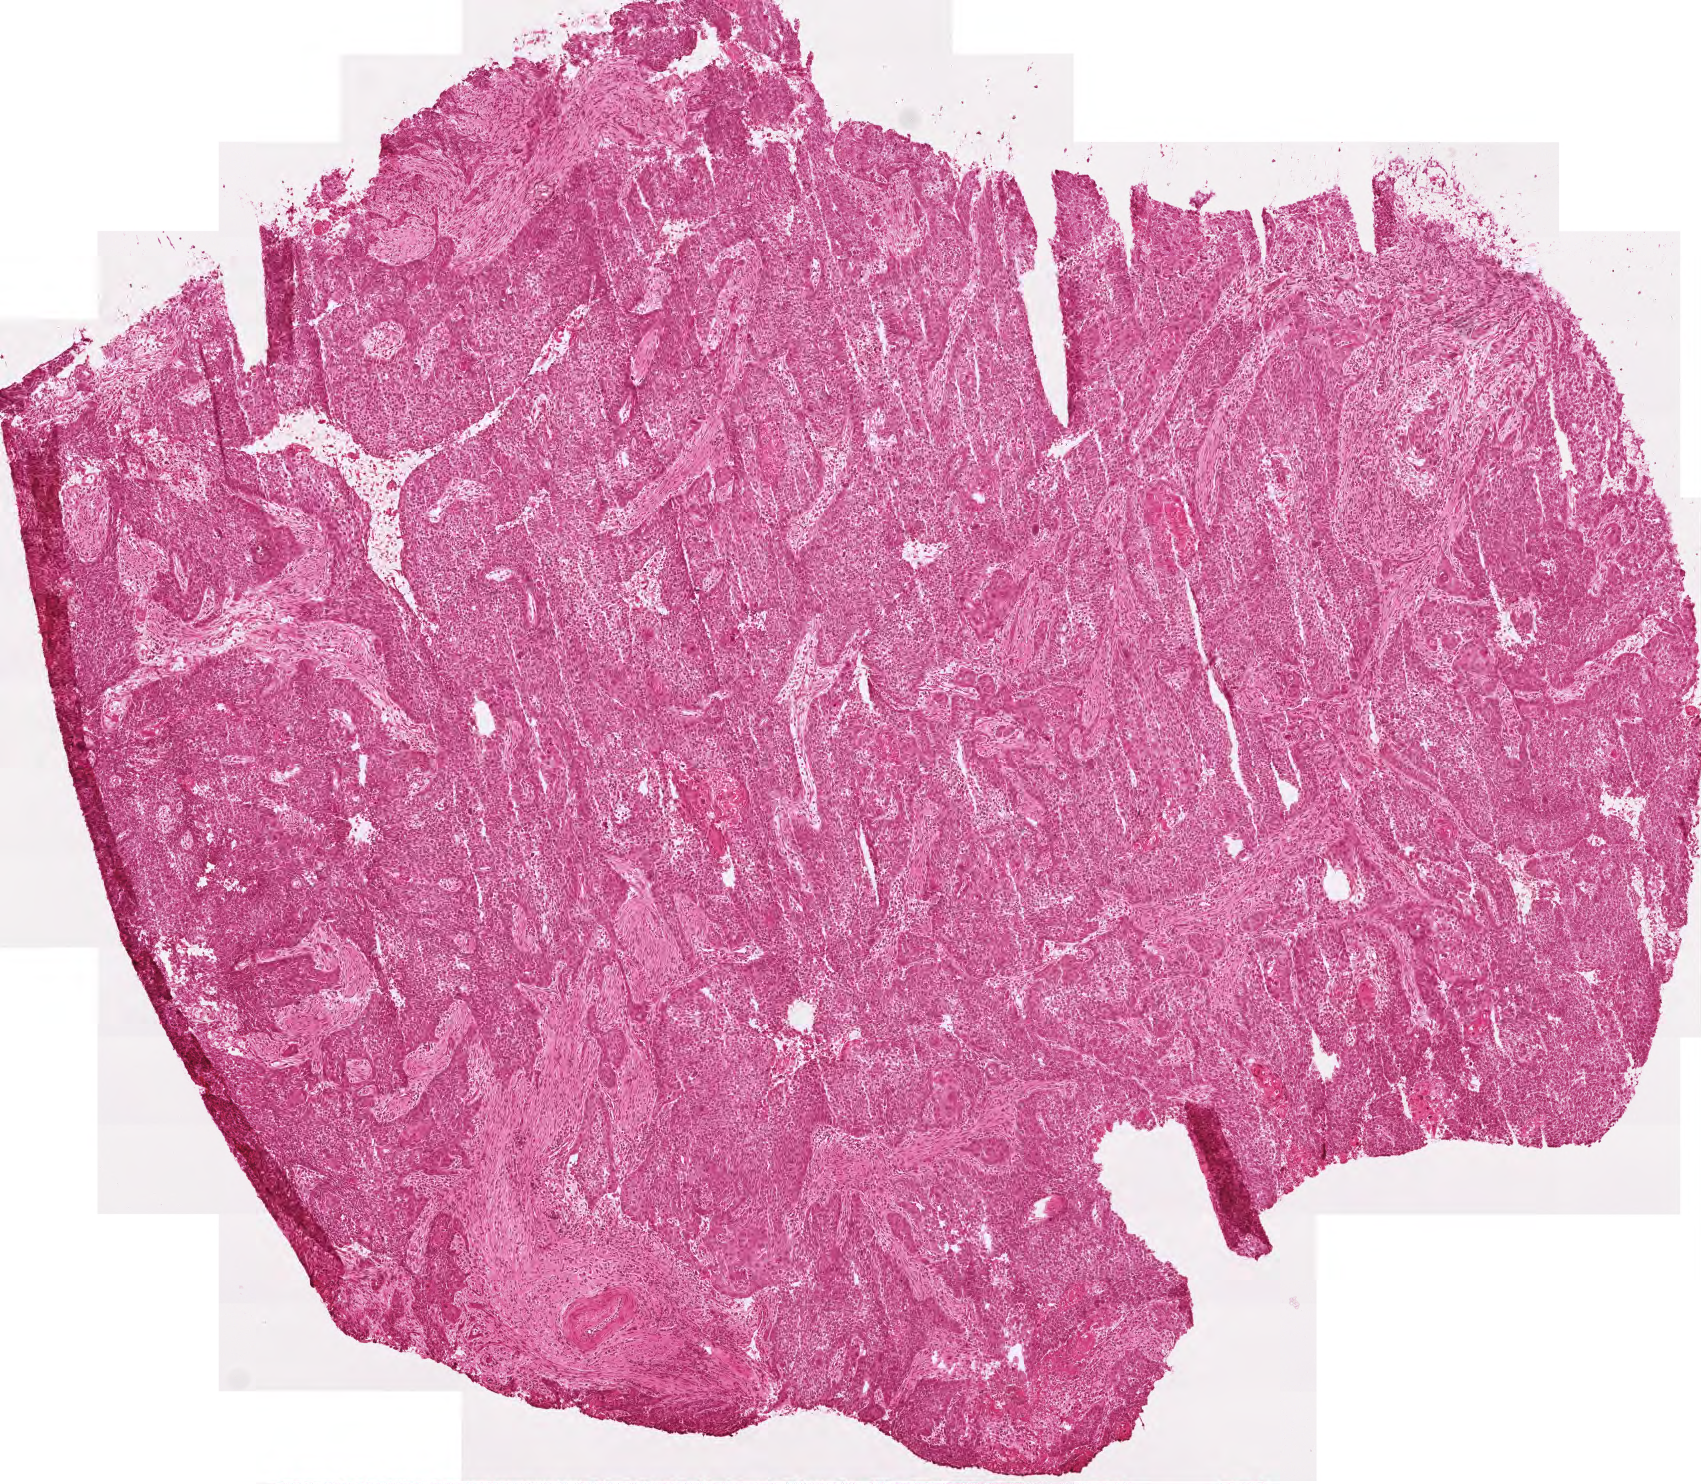
H&E-stained whole-slide image — whole scanned area (about 3.4 x 3.0 mm) shown as a low-resolution overview; frozen section from the top of the tissue portion; sample: primary tumour, head and neck. Patient: female, age at initial diagnosis 53 years. Histologic grade: G2 (moderately differentiated). Slide review estimates, as recorded: tumour cells 100%, tumour nuclei 80%, normal cells 0%, stromal cells 0%, necrosis 0%. Inflammatory infiltration, as recorded: lymphocyte infiltration 15%, monocyte infiltration 0%, neutrophil infiltration 0%.
• lymph nodes positive (case pathology): 0 of 23 examined
• histologic diagnosis: Squamous cell carcinoma, NOS (larynx, NOS)
• AJCC pathologic stage: II